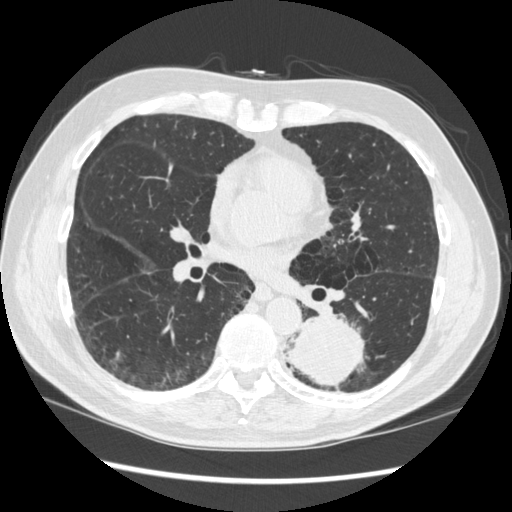
Low-dose screening chest CT, one axial slice. Position 156 of 348 along the scan axis. Reconstruction kernel STANDARD. 120 kVp. Lung window (W 1500 / L -600 HU). 1.25 mm slice thickness. 512 × 512 image matrix, field of view 360 × 360 mm.
Outlined on this slice (expert manual segmentation):
- lesion 1 (tumor, lower lobe of left lung): bounding box [x1, y1, x2, y2] px = [287, 315, 365, 387]